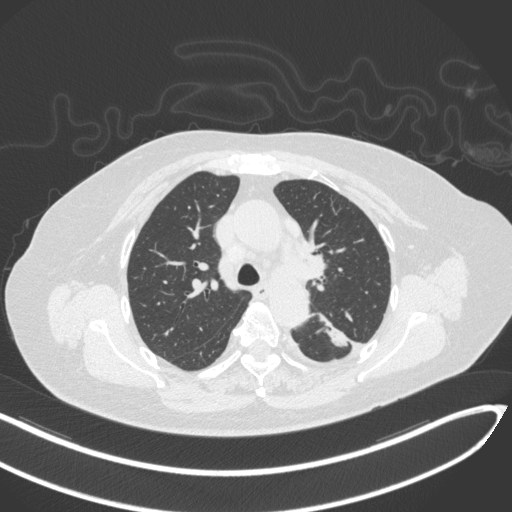
Chest CT, one axial slice; reconstruction kernel B31f; 120 kVp; lung window (W 1500 / L -600 HU); 1 mm slice thickness; 512 × 512 image matrix. Female patient, age 76 years. From the clinical record (not read from this slice): clinical TNM (as recorded): T1c N0 M0.
Outlined on this slice (rectangle marked by the reading radiologist):
- lung tumour (recorded histology: adenocarcinoma): bounding box [x1, y1, x2, y2] px = [317, 313, 360, 353]